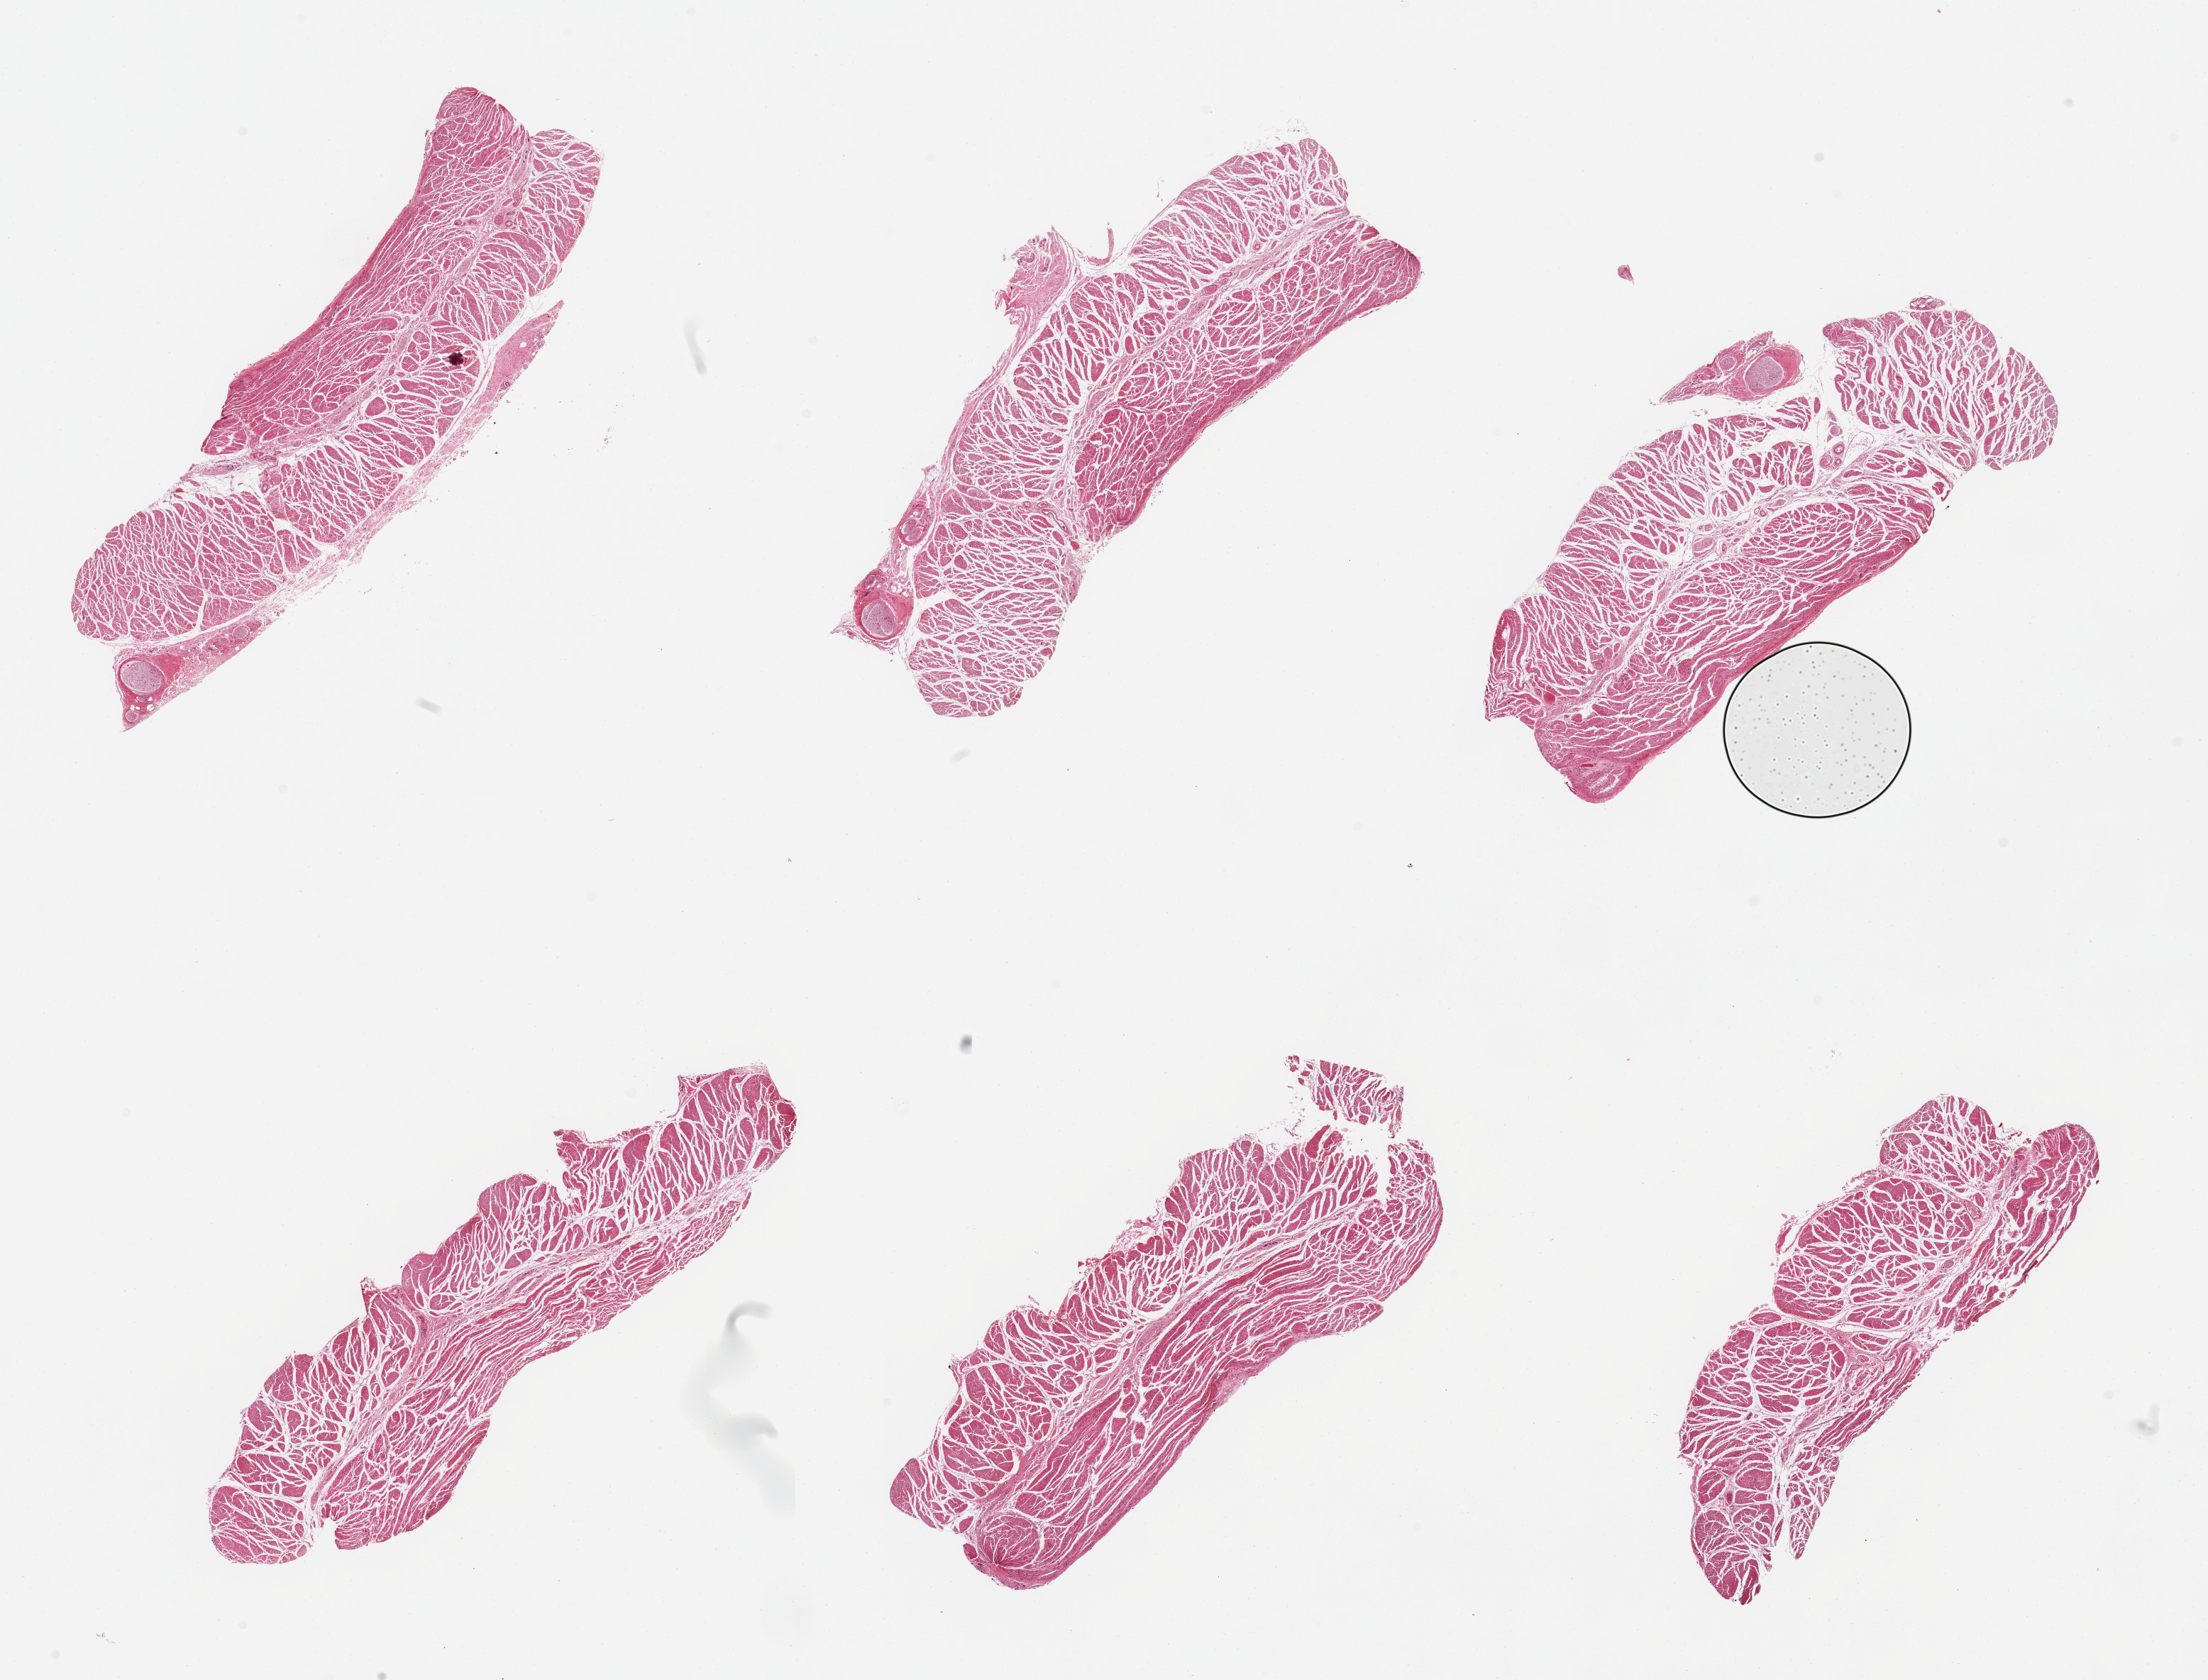
Haematoxylin and eosin whole-slide image, brightfield — a low-resolution overview of the entire scanned area, about 24.6 x 18.7 mm (from a 20x scan), PAXgene-fixed, paraffin-embedded tissue, section of esophageal muscle (target tissue), donor tissue sample. Donor: female.
Review note (as recorded): 6 pieces; target muscularis present, few pieces include portion of larger nerves.